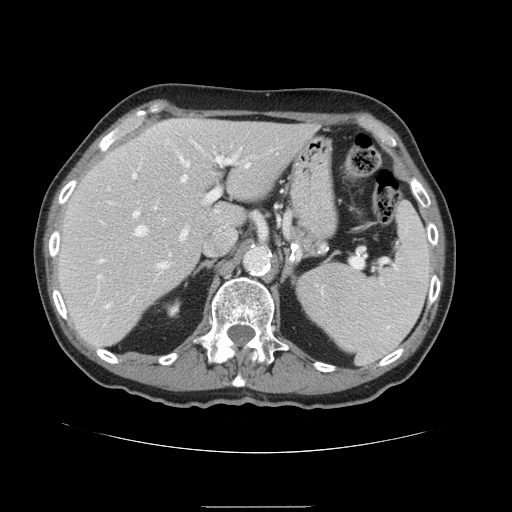
Contrast-enhanced abdominal CT, one axial slice. Slice 100 of 168 in the series (ordered by position). Soft-tissue window (W 400 / L 40 HU). 2.5 mm slice thickness. 512 × 512 image matrix, field of view 386 × 386 mm. Male patient, age 74 years. Case-level facts recorded for this patient, not image findings: diagnosis: colorectal cancer liver metastases, imaged before liver resection; multiple liver metastases: no; largest metastasis: 14.5 cm; disease in both lobes: yes.
Outlined on this slice (outlined manually by an expert reader):
- hepatic veins: box from (x=136, y=158) to (x=249, y=266) px
- liver: (x=57, y=118)–(x=318, y=347)
- planned liver remnant (the part of the liver to remain after resection): (x=57, y=120)–(x=318, y=347)
- portal vein (with intrahepatic branches): (x=97, y=156)–(x=235, y=238)